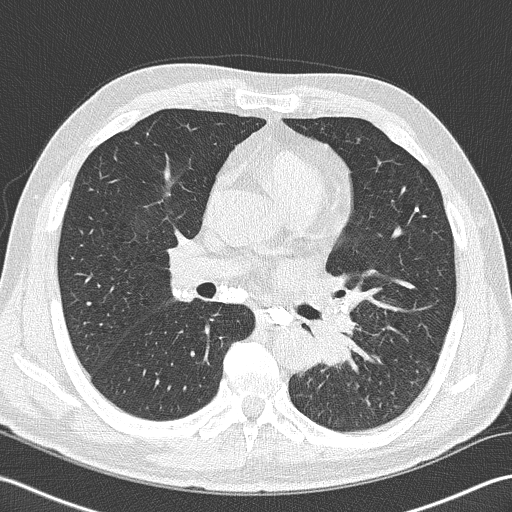
Axial slice from a low-dose chest CT screening exam, second annual screen, lung window (W 1500 / L -600 HU), 2 mm slice thickness, lung (sharp) reconstruction kernel (B50f), slice 75 of 170 in the series. Male, age 57 years at enrolment. Former smoker at enrolment.
- Expert reader's lesion annotation, bounding box (x1, y1, x2, y2) in pixels: (293, 301, 373, 381).
- Screening reader's record for this exam (one nodule recorded; not confirmed to be the boxed lesion): non-calcified nodule or mass ≥4 mm, left lower lobe, 40 × 30 mm, spiculated (stellate) margins, soft tissue attenuation, pre-existing on the prior screen: no.
- Official screen result: positive, other.
- Participant outcome: lung cancer diagnosed 9 days after this screen — squamous cell carcinoma, NOS, left lower lobe, moderately differentiated (G2), stage IIIB (AJCC 6th edition), 38 mm at pathology.